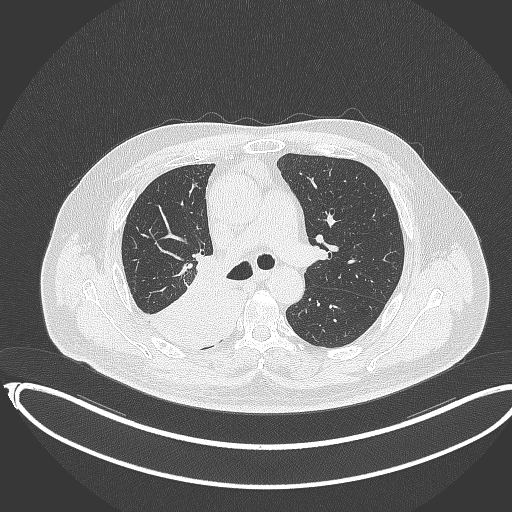
Chest CT, one axial slice; position 230 of 403 along the scan axis; 120 kVp; lung window (W 1500 / L -600 HU); 1 mm slice thickness; 512 × 512 image matrix, field of view 436 × 436 mm. Male patient, age 68 years. From the clinical record (not read from this slice): clinical TNM (as recorded): T2a N0 M0.
Annotated regions visible in this slice (rectangle marked by the reading radiologist):
- lung tumour (recorded histology: adenocarcinoma): bounding box (x1, y1, x2, y2) in pixels: (145, 256, 232, 349)